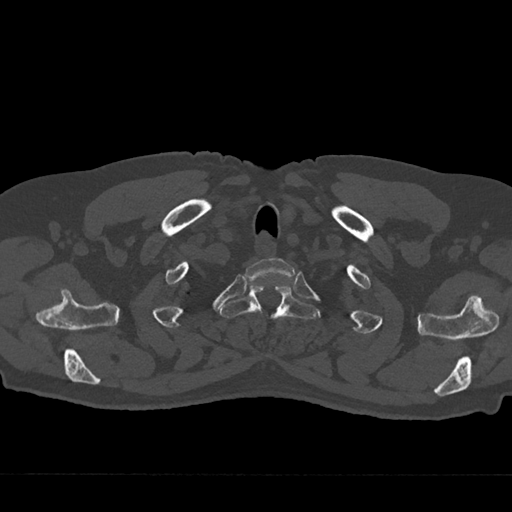
CT including the spine, one axial slice. Slice 627 of 797 in the series (ordered by position). Reconstruction kernel Br40s/3. Bone window (W 1800 / L 400 HU). 0.5 mm slice thickness. 512 × 512 image matrix, field of view 377 × 377 mm. Patient: male, 75 years. From the clinical record (not read from this slice): primary cancer: renal; vertebrae with lytic lesions (as recorded): T4.
Annotated regions visible in this slice (semi-automatic segmentation, software-assisted and operator-edited):
- T1 vertebra: bounding box <245,258,294,282> (left, top, right, bottom; pixels)
- T2 vertebra: <220,286,319,320>